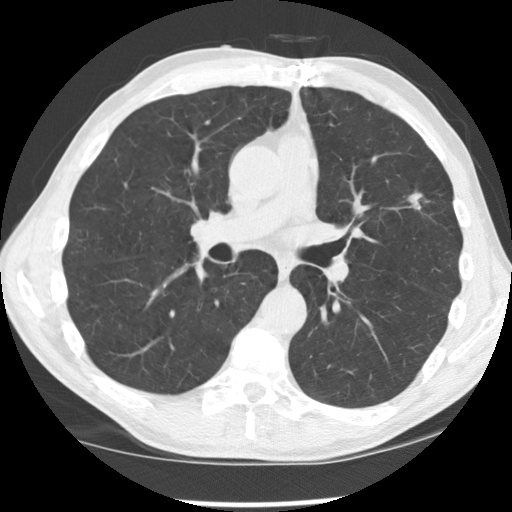
Axial slice from a low-dose chest CT screening exam, second annual screen, lung window (W 1500 / L -600 HU), 2.5 mm slice thickness, slice 75 of 170 in the series, 512 × 512 image matrix, field of view 340 × 340 mm. Male participant, aged 64 years at enrolment. Current smoker at enrolment.
• Lesion marked by an expert reader, bounding box <385,177,441,223> (left, top, right, bottom; pixels).
• Screening reader's record for this exam (one nodule recorded; not confirmed to be the boxed lesion): non-calcified nodule or mass ≥4 mm, left upper lobe, 16 × 11 mm, spiculated (stellate) margins, soft tissue attenuation, pre-existing on the prior screen: yes; interval growth: yes.